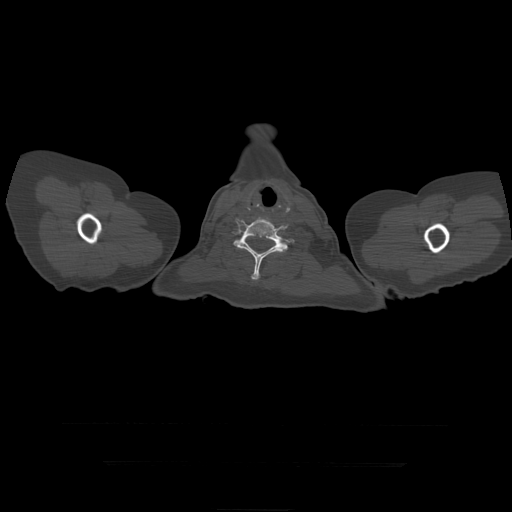
CT including the spine, one axial slice. Slice 399 of 399 in the series (ordered by position). Reconstruction kernel STANDARD. Bone window (W 1800 / L 400 HU). 512 × 512 image matrix, field of view 450 × 450 mm. Patient age 41 years. Case-level facts recorded for this patient, not image findings: primary cancer: breast.
Annotated regions visible in this slice (semi-automatically segmented with operator editing):
- T1 vertebra: bounding box <233,236,253,250> (left, top, right, bottom; pixels)